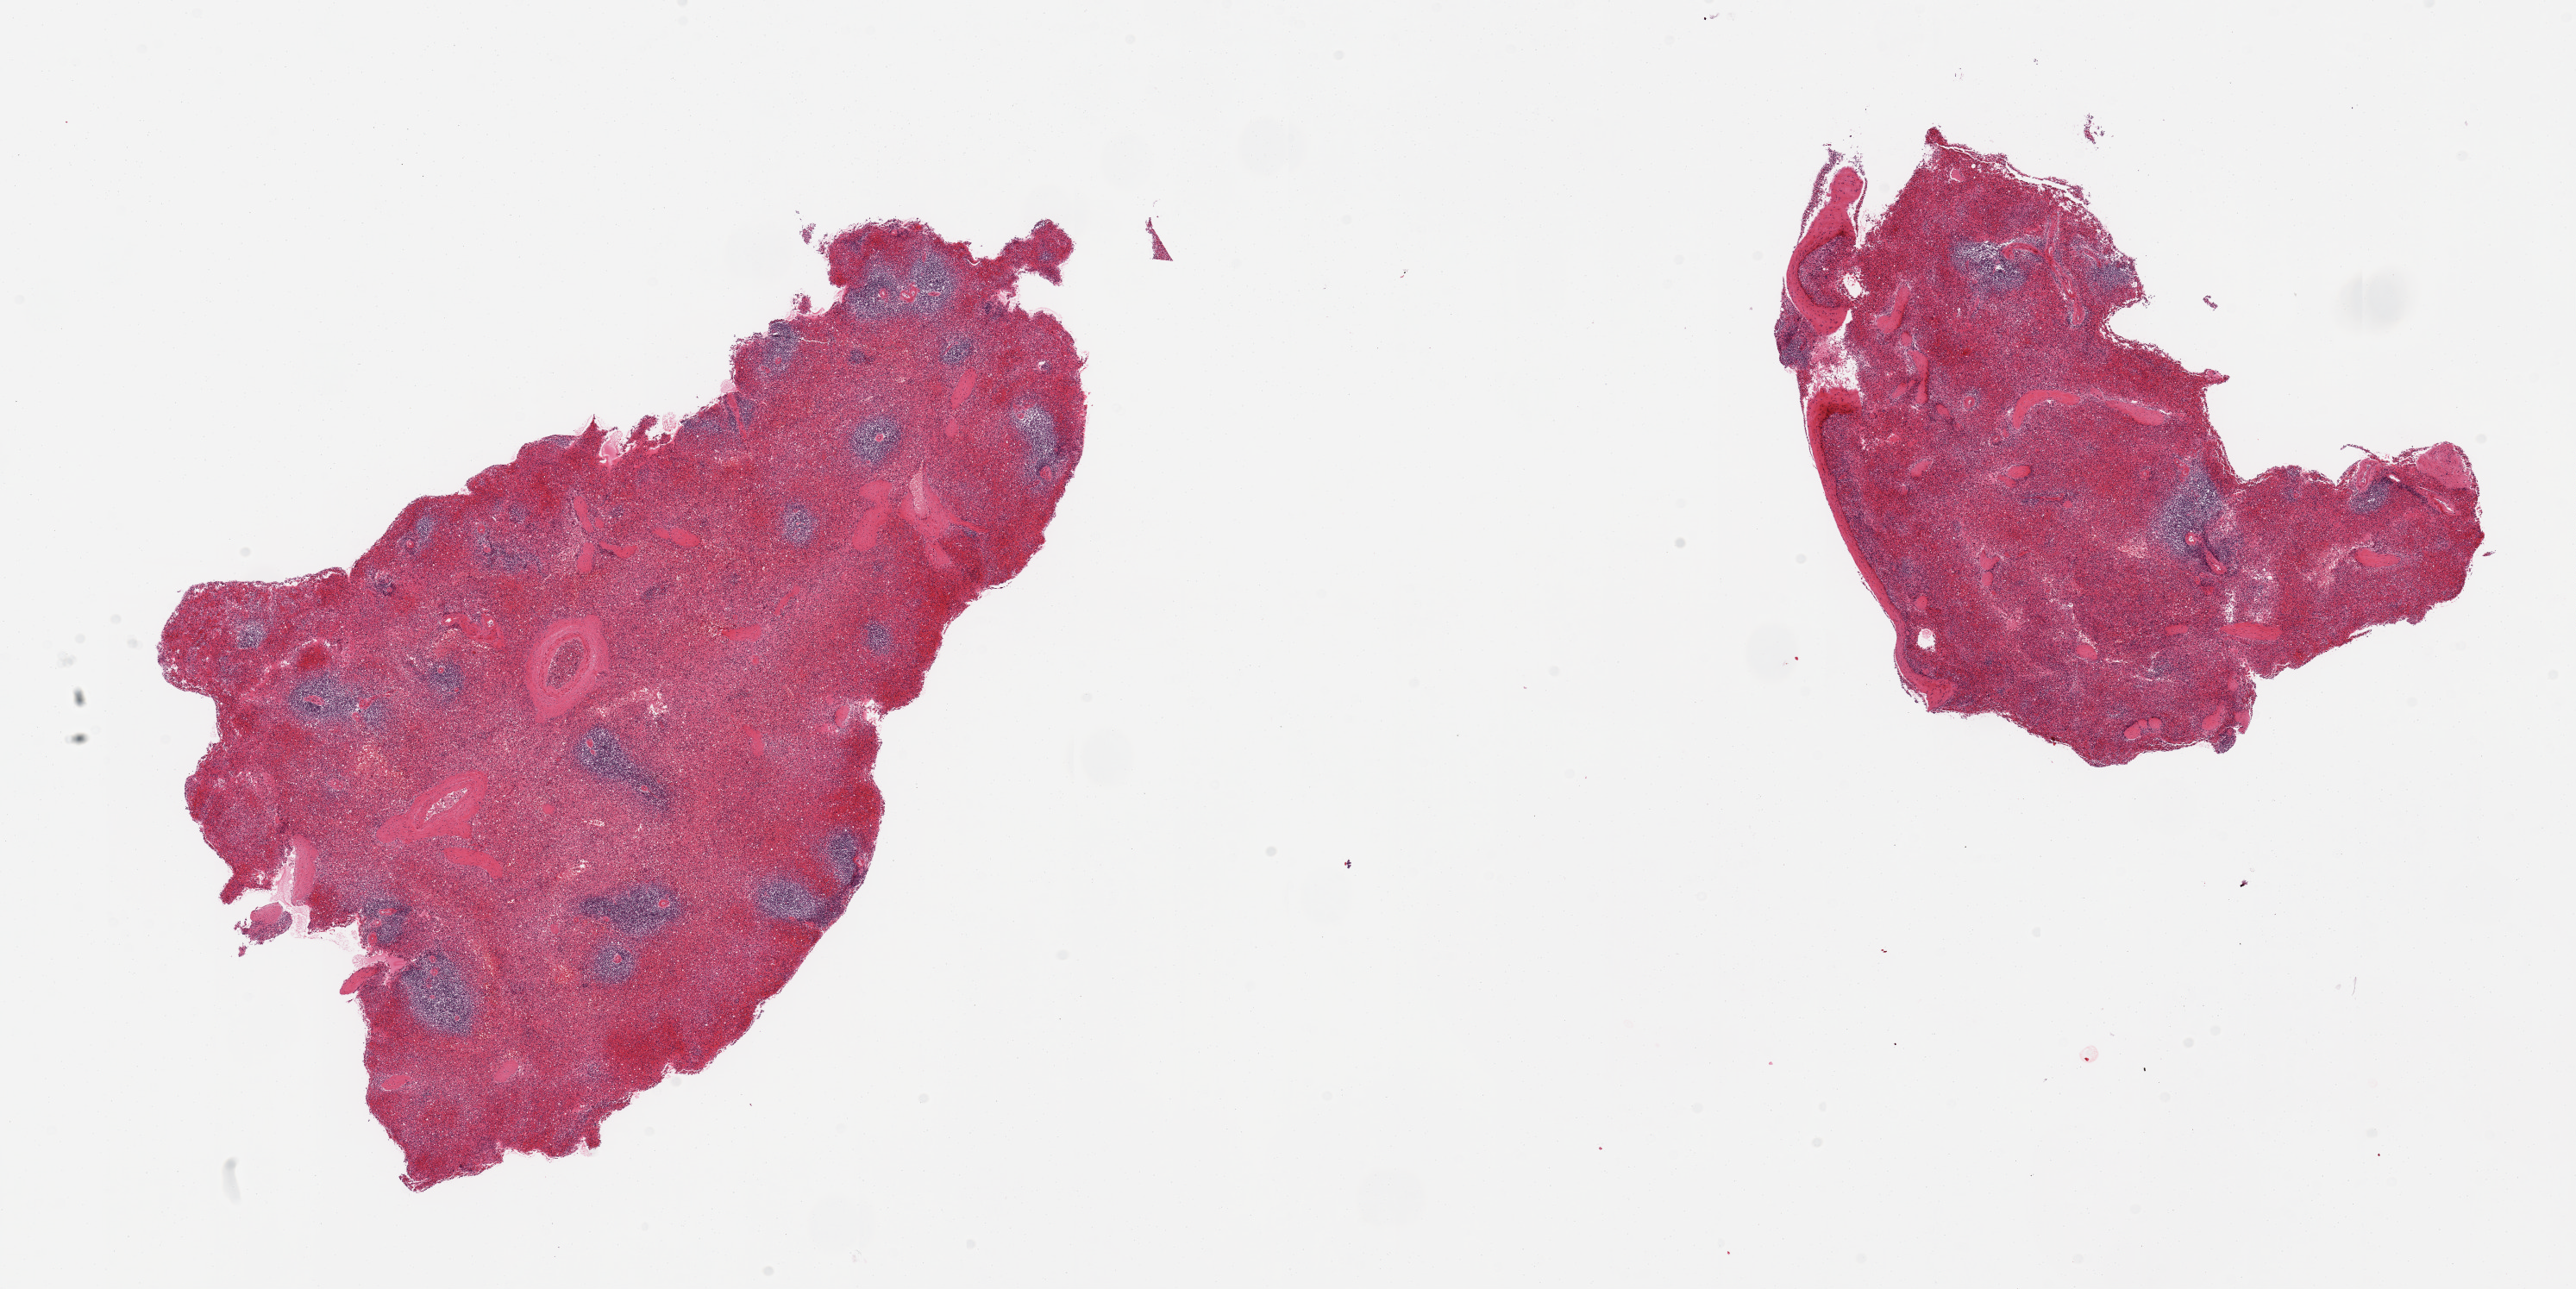
Haematoxylin and eosin whole-slide image, shown as a low-resolution overview of the whole scanned area (about 23.6 x 11.8 mm), PAXgene-fixed paraffin-embedded (PFPE) section, section of spleen (target tissue), tissue donor sample.
- review note (as recorded): 2 pieces; moderate vascular congestion